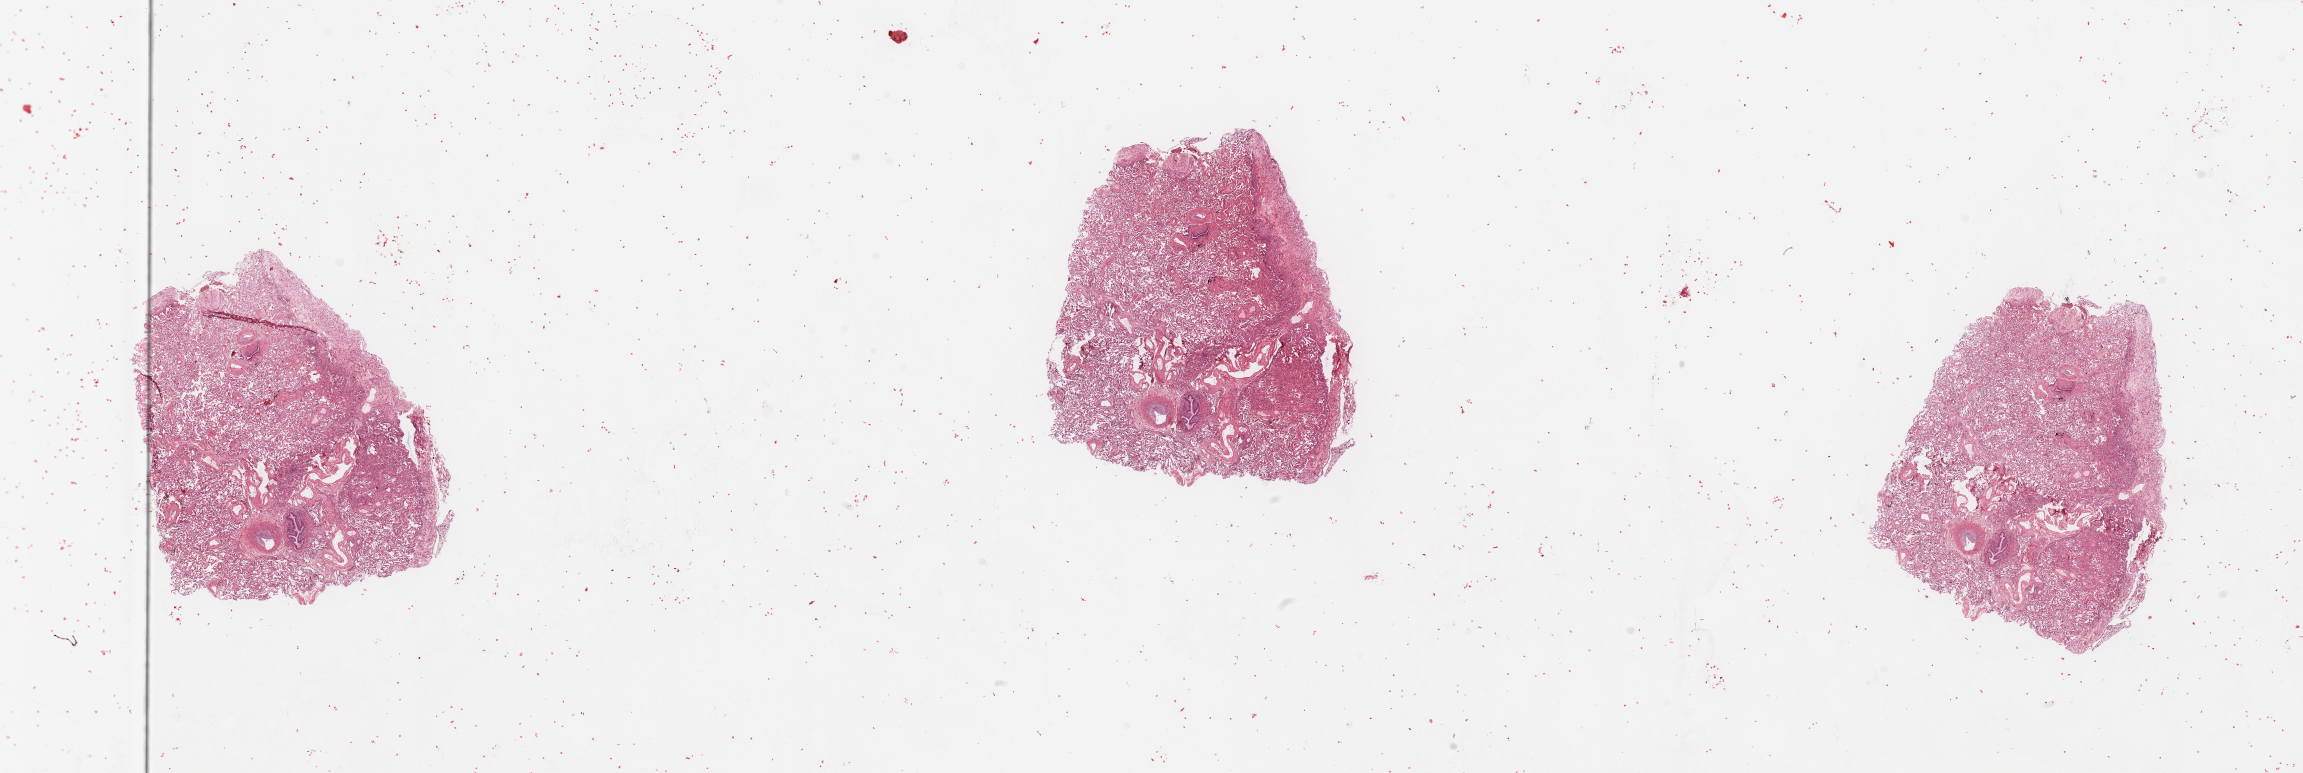
Hematoxylin and eosin (H&E) stained whole-slide image — shown as a low-resolution overview of the whole scanned area (about 36.4 x 12.2 mm, from a 20x scan), normal (non-tumour) tissue sample, sampled site: lung. Male, 70 y/o.
This section: normal (non-tumour) tissue from the same patient. Patient diagnosis: Squamous cell carcinoma, NOS.